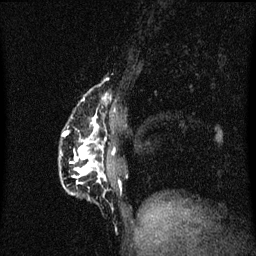
Breast MRI (dynamic contrast-enhanced), one sagittal slice. Position 16 of 60 along the scan axis. Dynamic contrast-enhanced series, image 2 of 3 at this slice position (ordered by acquisition). 1.5 T. TE 4.2 ms, TR 8.4 ms. 2 mm slice thickness. 256 × 256 image matrix, field of view 200 × 200 mm. Female patient, age 40 years.
Annotated regions visible in this slice (semi-automatically segmented with operator editing):
- analysis volume of interest (the breast-tissue region the enhancement analysis was run in; not a lesion): bounding box [x1, y1, x2, y2] px = [60, 86, 111, 201]
- tumour enhancement mask (voxels above the 70 % enhancement threshold inside the analysis volume of interest): [63, 116, 107, 185]